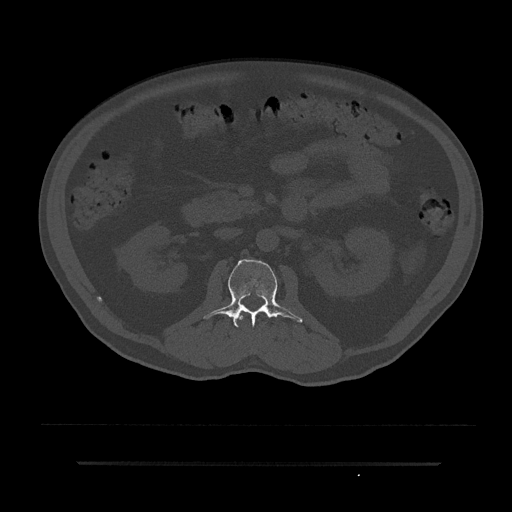
CT including the spine, one axial slice; position 82 of 797 along the scan axis; reconstruction kernel Br40s/3; 120 kVp; bone window (W 1800 / L 400 HU); 0.5 mm slice thickness; 512 × 512 image matrix, field of view 464 × 464 mm. Patient: male, 59 years. From the clinical record (not read from this slice): primary cancer: bile ducts; vertebrae with lytic lesions (as recorded): T10.
Annotated regions visible in this slice (semi-automatically segmented with operator editing):
- L1 vertebra: box from (x=236, y=311) to (x=244, y=326) px
- L2 vertebra: (x=203, y=259)–(x=303, y=328)